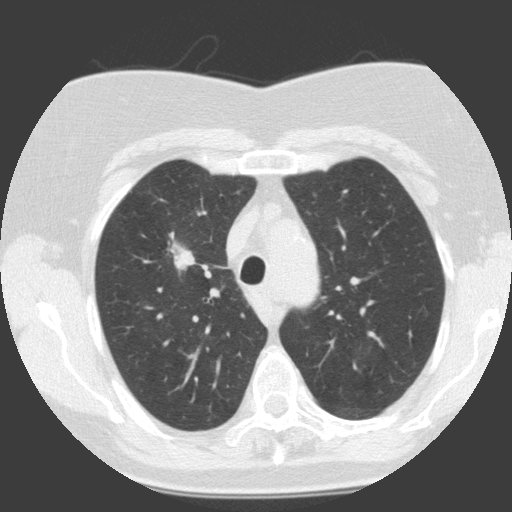
Axial slice from a low-dose chest CT screening exam, baseline annual screen, lung window (W 1500 / L -600 HU), 2 mm slice thickness, slice 41 of 146 in the series, 512 × 512 image matrix, field of view 300 × 300 mm. Female, age 68 years at enrolment. Current smoker at enrolment.
Expert-annotated lung lesion, bounding box [x1, y1, x2, y2] px = [156, 233, 209, 281]. Reader record for this screening exam (exam-level; its link to the box is not recorded): non-calcified nodule or mass ≥4 mm, right upper lobe, 19 × 12 mm, smooth margins, soft tissue attenuation. Official screen result: positive, change unspecified: nodule(s) >= 4 mm or enlarging nodule(s), mass(es), or other non-specific abnormalities suspicious for lung cancer. Lung cancer was diagnosed 30 days after this screen: squamous cell carcinoma, NOS, right upper lobe, moderately differentiated (G2), stage IA (AJCC 6th edition), 28 mm at pathology.